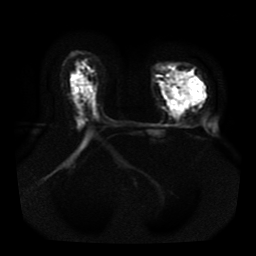
Breast MRI, one axial slice. Slice 27 of 41 in the series (ordered by position). Diffusion-weighted series; image 2 of 4 stored at this slice position (different b-values; order by instance number). 1.5 T. 5 mm slice thickness. 256 × 256 image matrix, field of view 330 × 330 mm. Female patient.
Outlined on this slice (outlined manually by an expert reader):
- tumour on diffusion-weighted imaging: bounding box [x1, y1, x2, y2] px = [160, 73, 205, 117]